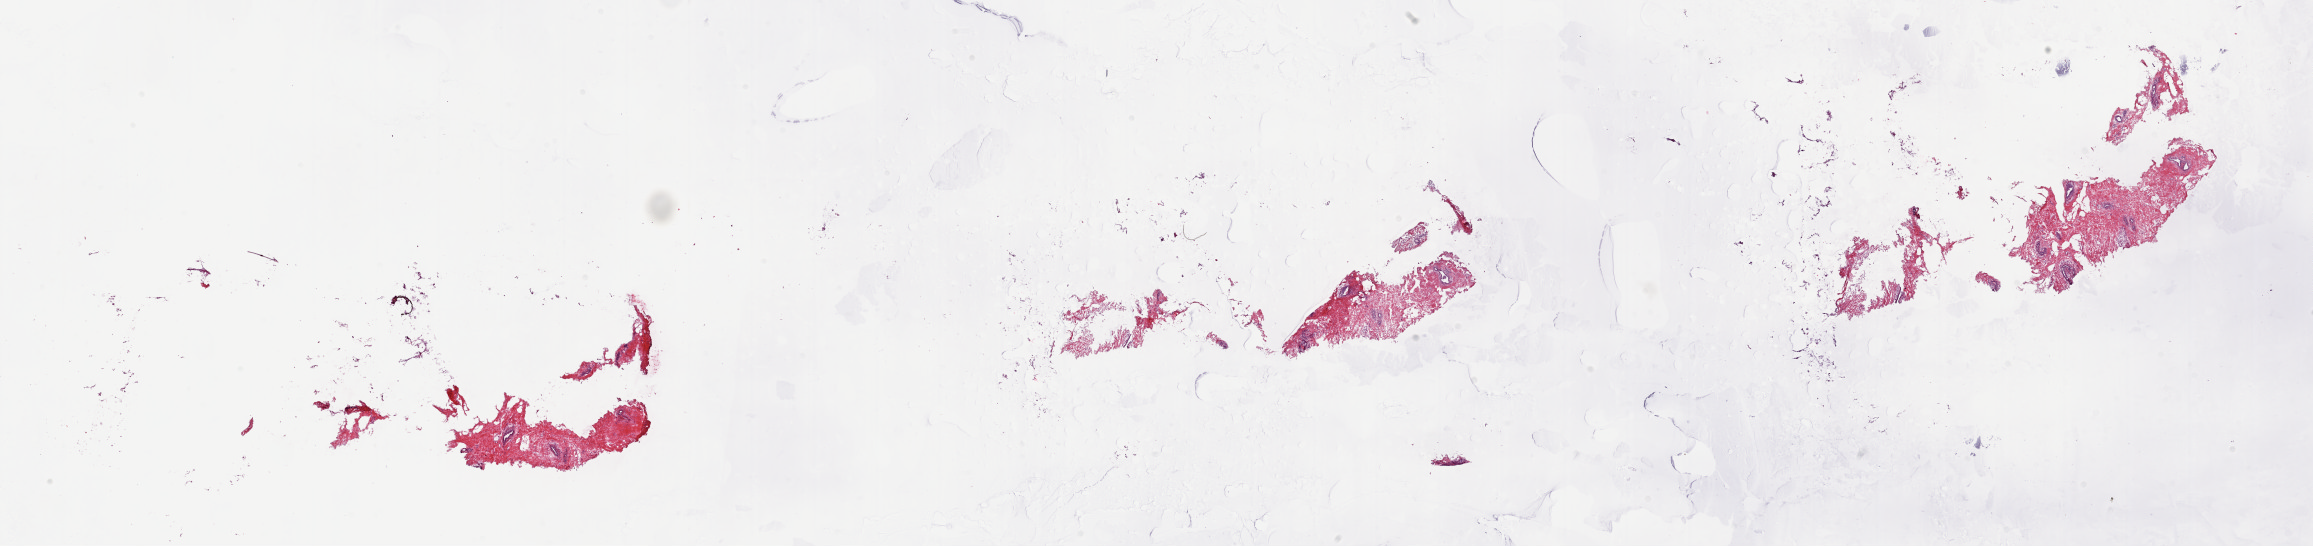
H&E-stained whole-slide image — a low-resolution overview of the entire scanned area, about 36.7 x 8.7 mm (from a 20x scan), frozen section from the top of the tissue portion, solid tissue normal (non-tumour tissue) sample from the breast. Female, age 62 years at initial diagnosis.
This section: solid tissue normal (non-tumour) sample from the same patient. Patient diagnosis: Lobular carcinoma, NOS.